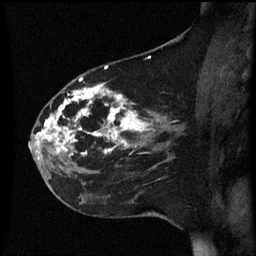
Breast MRI (dynamic contrast-enhanced), one sagittal slice. Position 24 of 60 along the scan axis. Dynamic contrast-enhanced series, image 2 of 3 at this slice position (ordered by acquisition). 1.5 T. TE 4.2 ms, TR 8.4 ms. 2.2 mm slice thickness. 256 × 256 image matrix. Female patient, age 35 years. From the clinical record (not read from this slice): setting: breast cancer imaged before/during neoadjuvant chemotherapy; receptor status: HER2-positive.
Structures marked on this image (semi-automatic segmentation, software-assisted and operator-edited):
- analysis volume of interest (the breast-tissue region the enhancement analysis was run in; not a lesion): bounding box (x1, y1, x2, y2) in pixels: (32, 78, 173, 163)
- tumour enhancement mask (voxels above the 70 % enhancement threshold inside the analysis volume of interest): (37, 78, 151, 155)